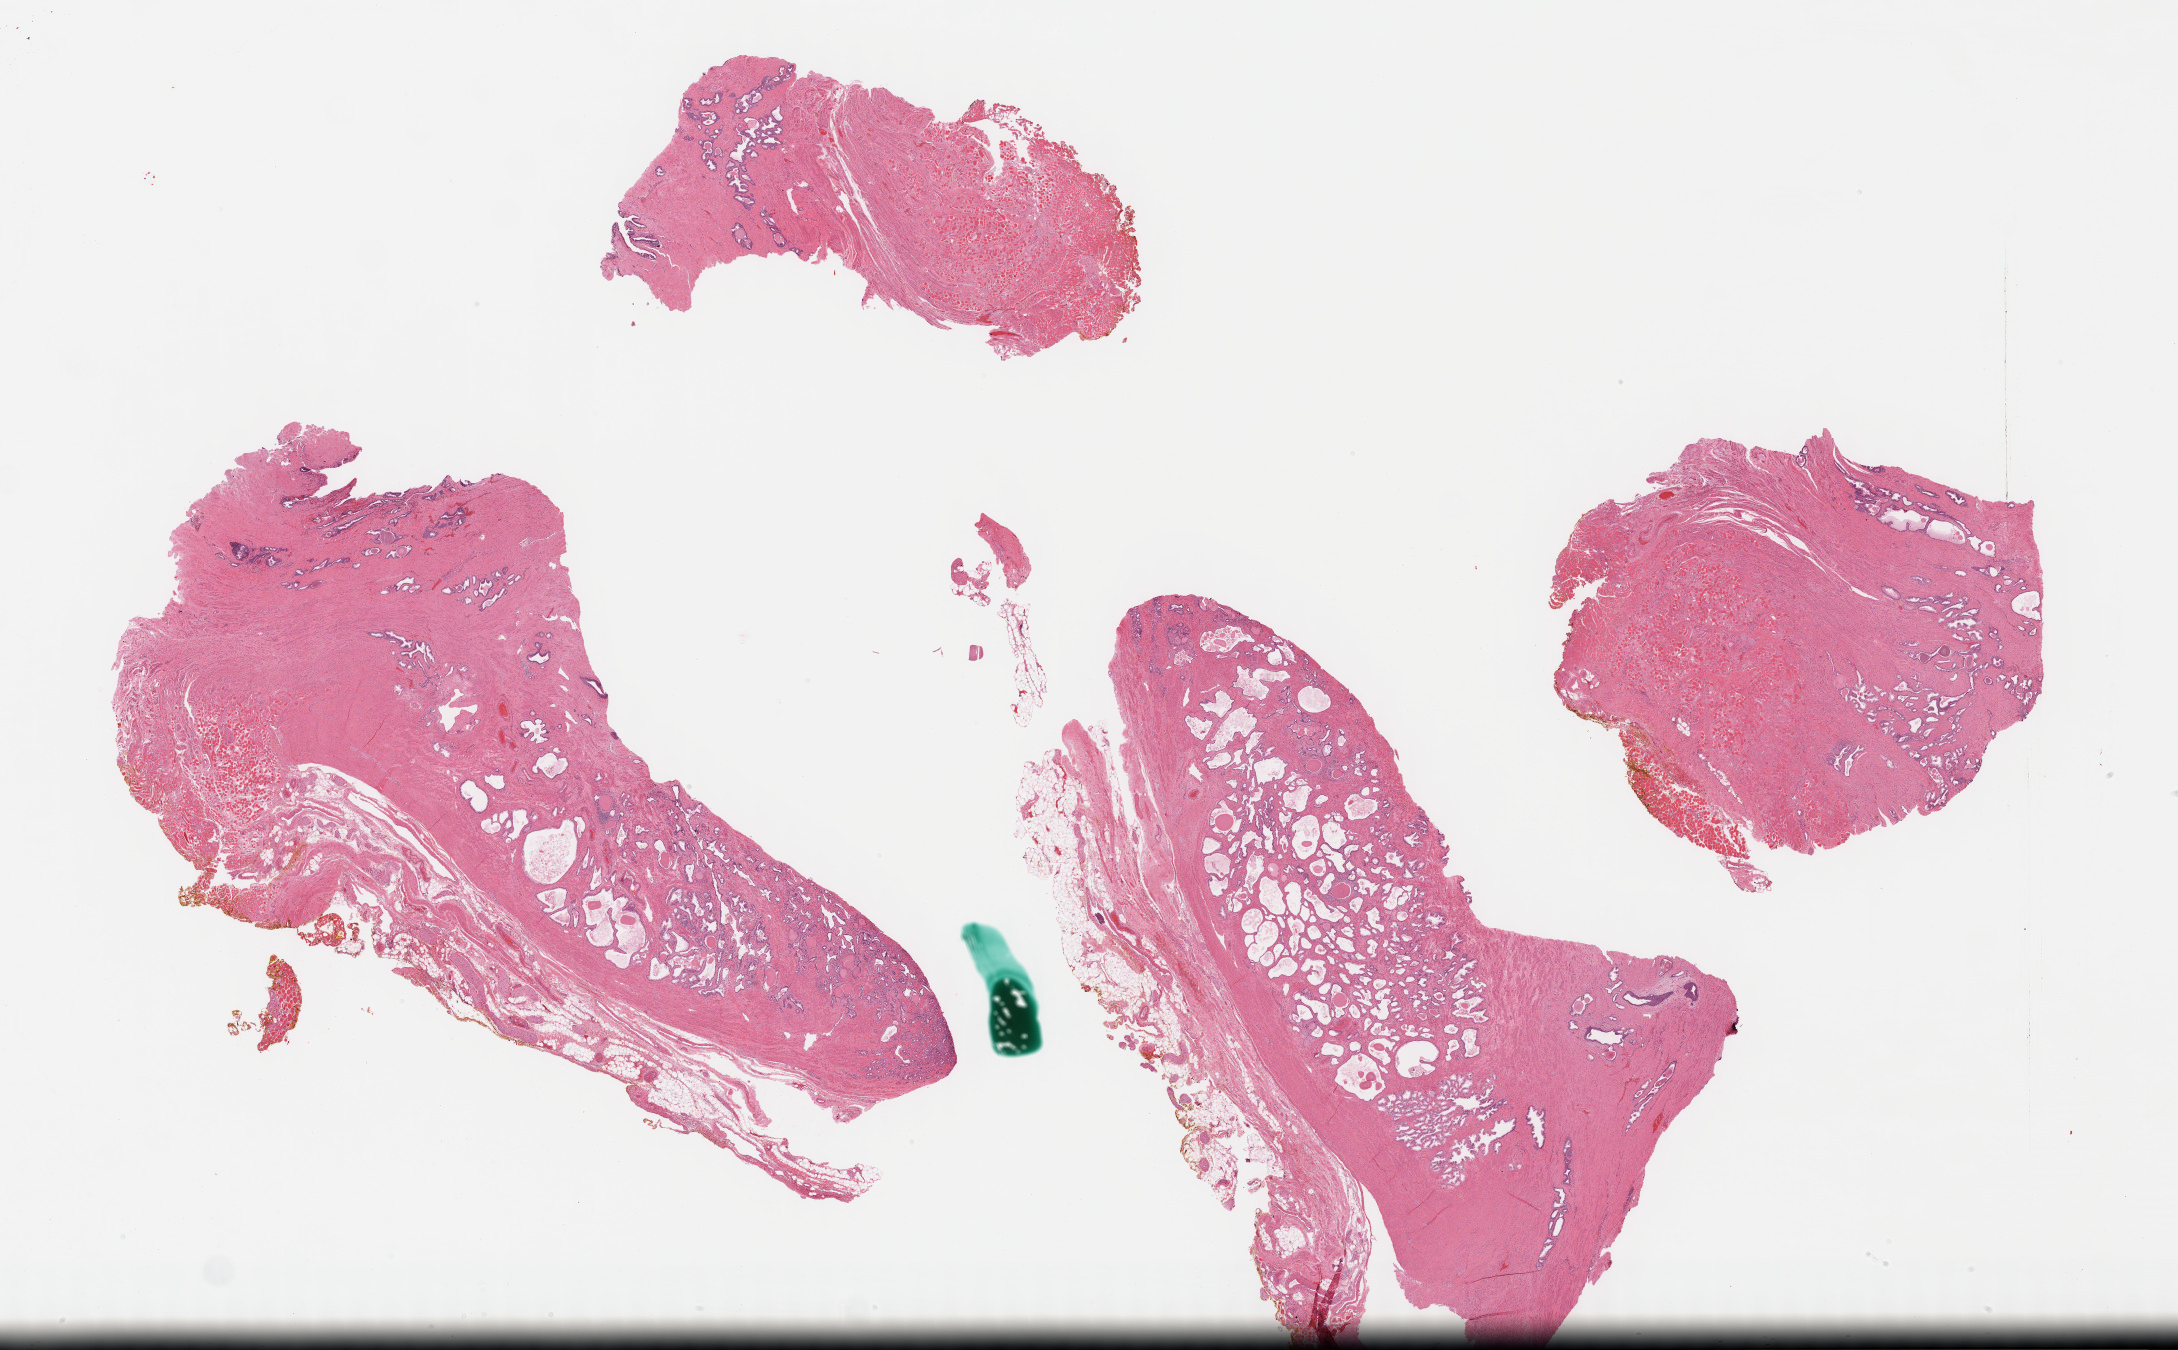
Whole-slide histology image, Hematoxylin and eosin (H&E) stained — a low-resolution overview of the entire scanned area, about 35.2 x 21.8 mm (acquisition: 40x scan). Formalin-fixed paraffin-embedded (FFPE) diagnostic section. Primary tumour sample from the prostate. Male, age 61 years at initial diagnosis. Gleason score: 7 (3+4).
Pathologic diagnosis: Adenocarcinoma, NOS (prostate gland). Laterality: bilateral.